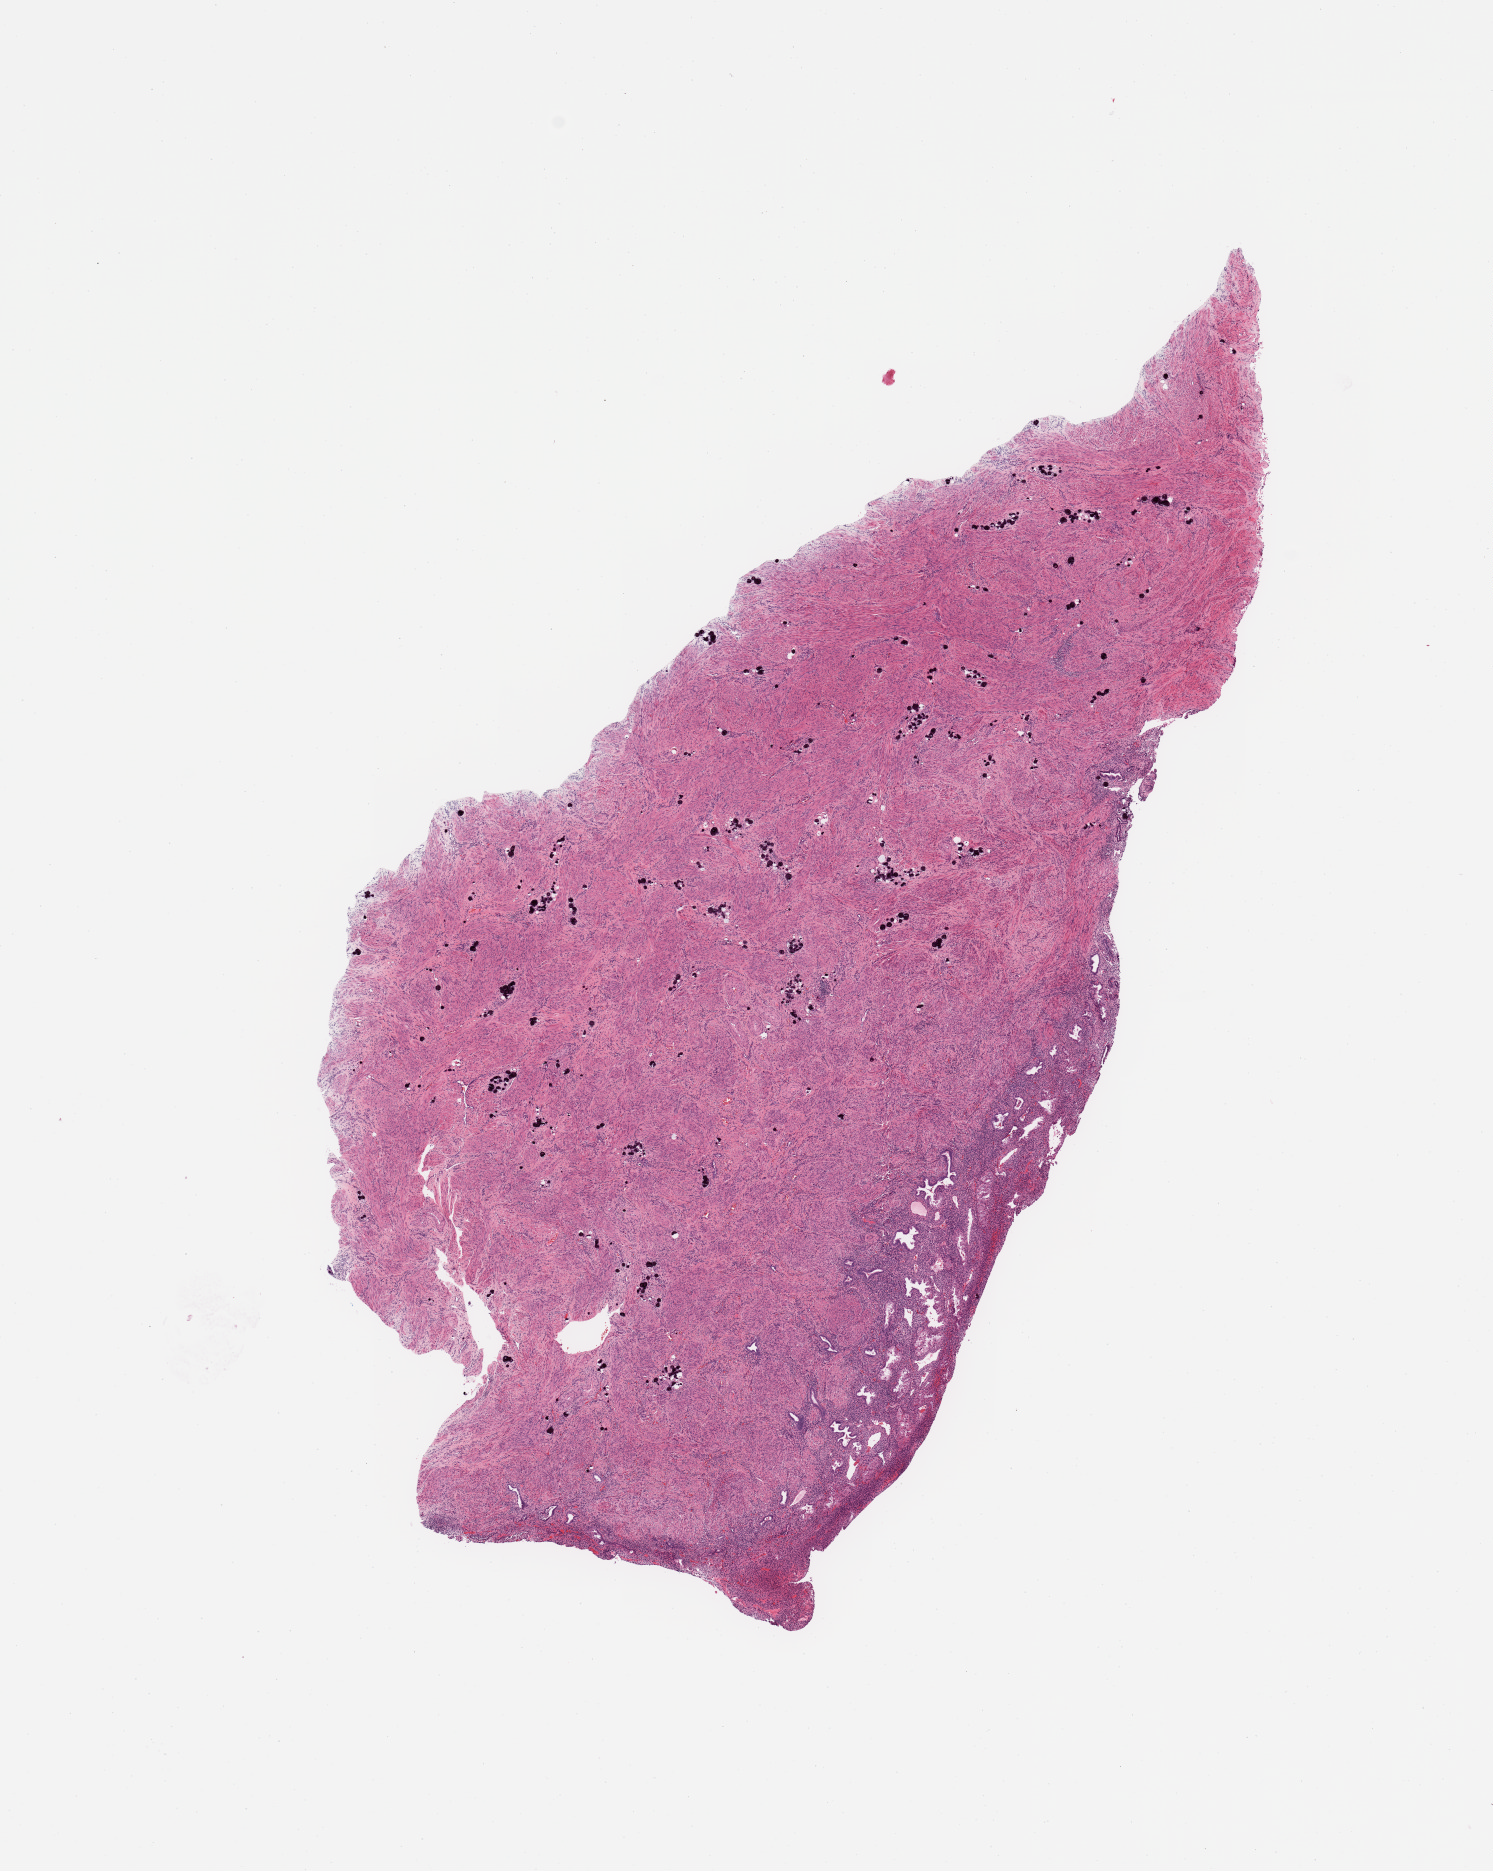
Digitized H&E-stained tissue section (whole slide) — low-resolution overview of the scanned area, about 11.8 x 14.8 mm, normal (non-tumour) tissue sample, sampled site: uterus. Female, 50 y/o.
This section: normal (non-tumour) tissue from the same patient. Patient diagnosis: Endometrioid adenocarcinoma, NOS.